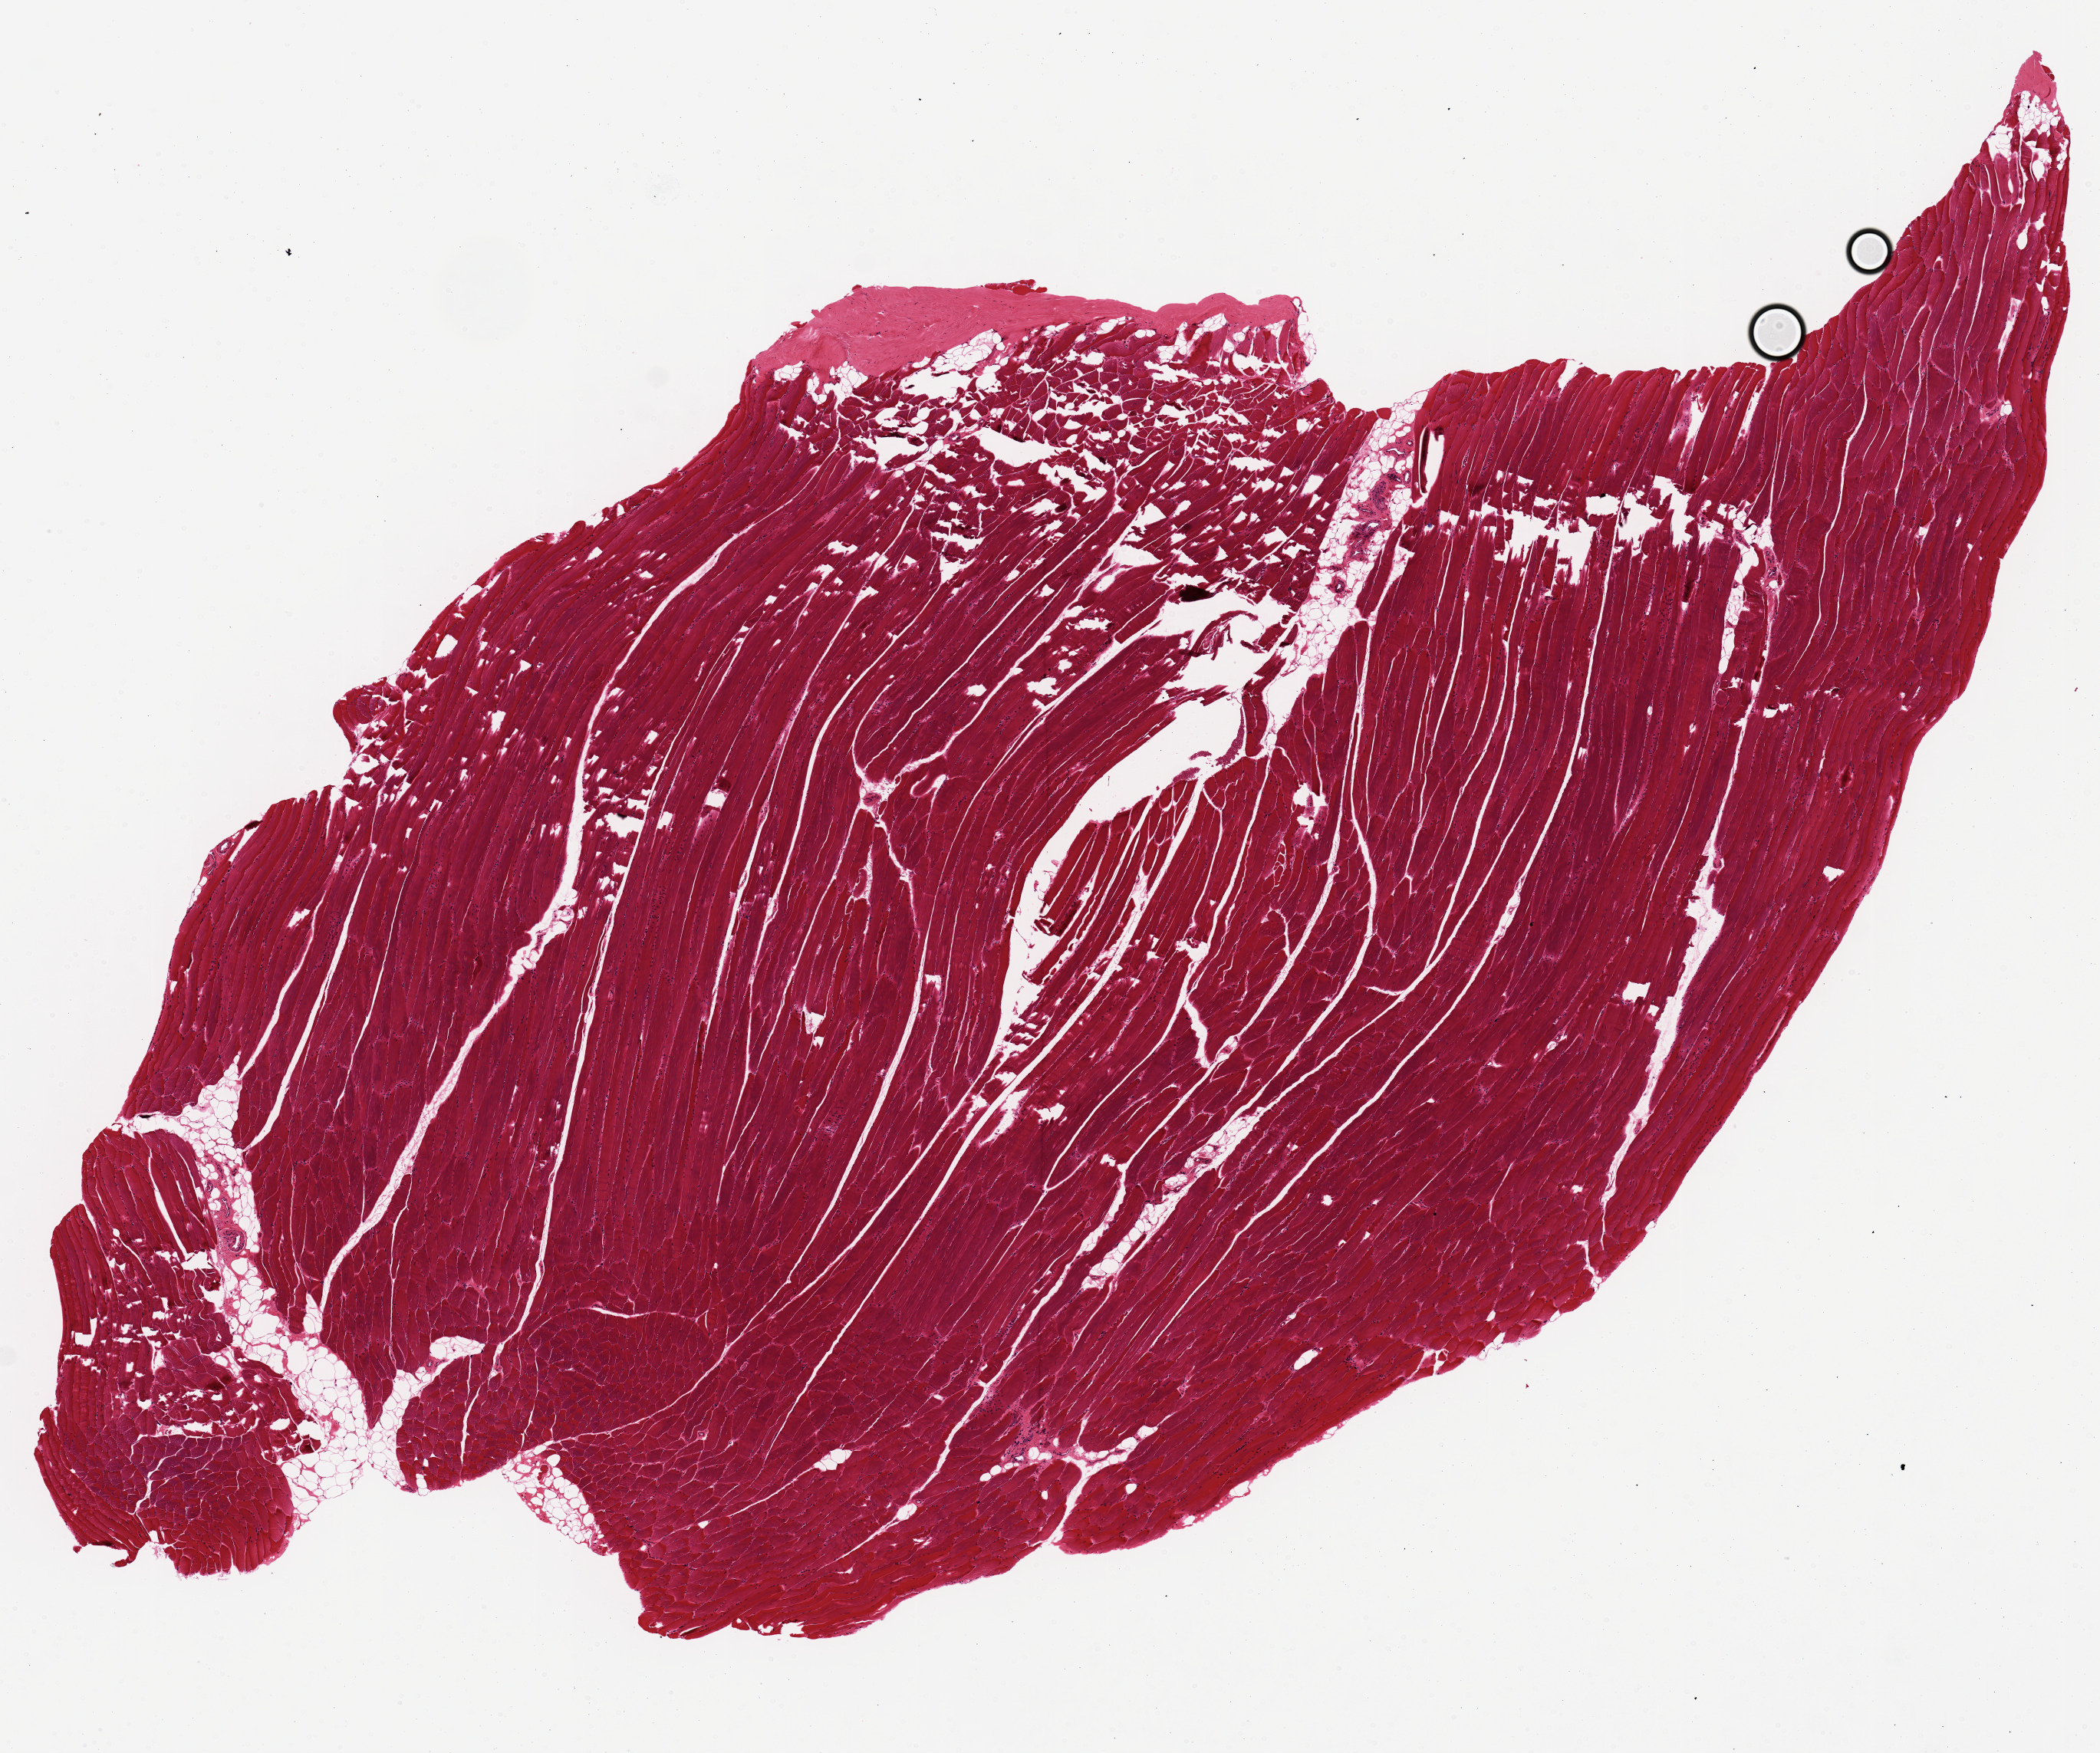
H&E whole-slide image, brightfield, shown as a low-resolution overview of the whole scanned area (about 10.8 x 9.0 mm, acquisition: 20x scan). PAXgene-fixed paraffin-embedded (PFPE) section. Target tissue: skeletal muscle. Tissue donor sample.
• pathologist's review note for this sample: Minimal interstitial fat